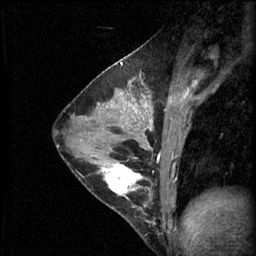
Breast MRI (dynamic contrast-enhanced), one sagittal slice. Slice 33 of 60 in the series (ordered by position). 3 images stored at this slice position (order not interpretable as contrast timing). 1.5 T. TE 4.2 ms, TR 11 ms. 256 × 256 image matrix, field of view 180 × 180 mm. Patient: female, 29 years.
Structures marked on this image (semi-automatically segmented with operator editing):
- analysis volume of interest (the breast-tissue region the enhancement analysis was run in; not a lesion): bounding box [x1, y1, x2, y2] px = [93, 164, 153, 227]
- tumour enhancement mask (voxels above the 70 % enhancement threshold inside the analysis volume of interest): [101, 164, 142, 195]